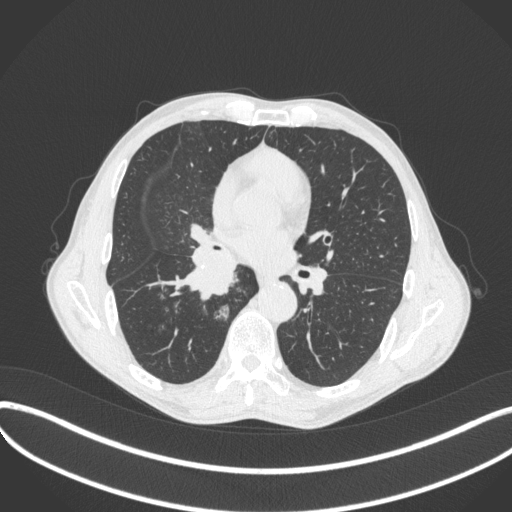
Chest CT, one axial slice. Slice 221 of 481 in the series (ordered by position). Lung window (W 1500 / L -600 HU). 1 mm slice thickness. 512 × 512 image matrix. Patient: male, 65 years. From the clinical record (not read from this slice): clinical TNM (as recorded): T2a N0 M0; histopathological grade: G2.
Structures marked on this image (bounding box drawn by a radiologist):
- lung tumour (recorded histology: squamous cell carcinoma): bounding box (x1, y1, x2, y2) in pixels: (182, 240, 243, 300)